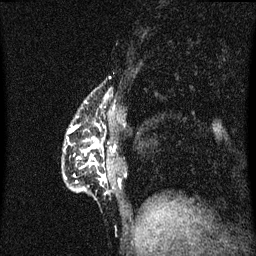
Breast MRI (dynamic contrast-enhanced), one sagittal slice; position 14 of 60 along the scan axis; dynamic contrast-enhanced series, image 2 of 3 at this slice position (ordered by acquisition); 1.5 T; TE 4.2 ms, TR 8.4 ms; 256 × 256 image matrix. Patient: female, 40 years.
Outlined on this slice (semi-automatic segmentation, software-assisted and operator-edited):
- analysis volume of interest (the breast-tissue region the enhancement analysis was run in; not a lesion): box from (x=63, y=102) to (x=109, y=199) px
- tumour enhancement mask (voxels above the 70 % enhancement threshold inside the analysis volume of interest): (x=70, y=124)–(x=106, y=183)